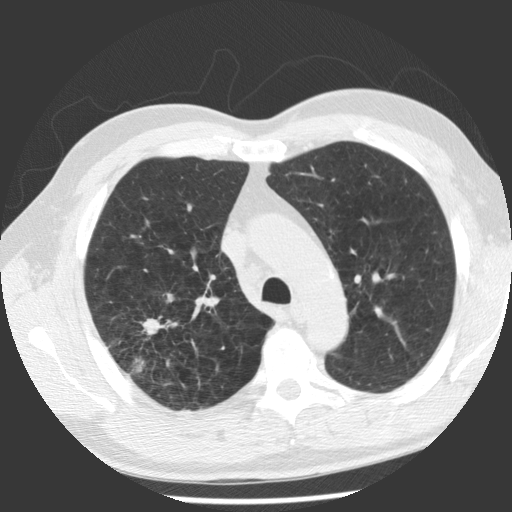
Low-dose screening chest CT, one axial slice; position 81 of 112 along the scan axis; reconstruction kernel STANDARD; 140 kVp; lung window (W 1500 / L -600 HU); 512 × 512 image matrix.
Structures marked on this image (expert manual segmentation):
- lesion 1 (tumor, upper lobe of right lung): bounding box (x1, y1, x2, y2) in pixels: (142, 319, 161, 335)